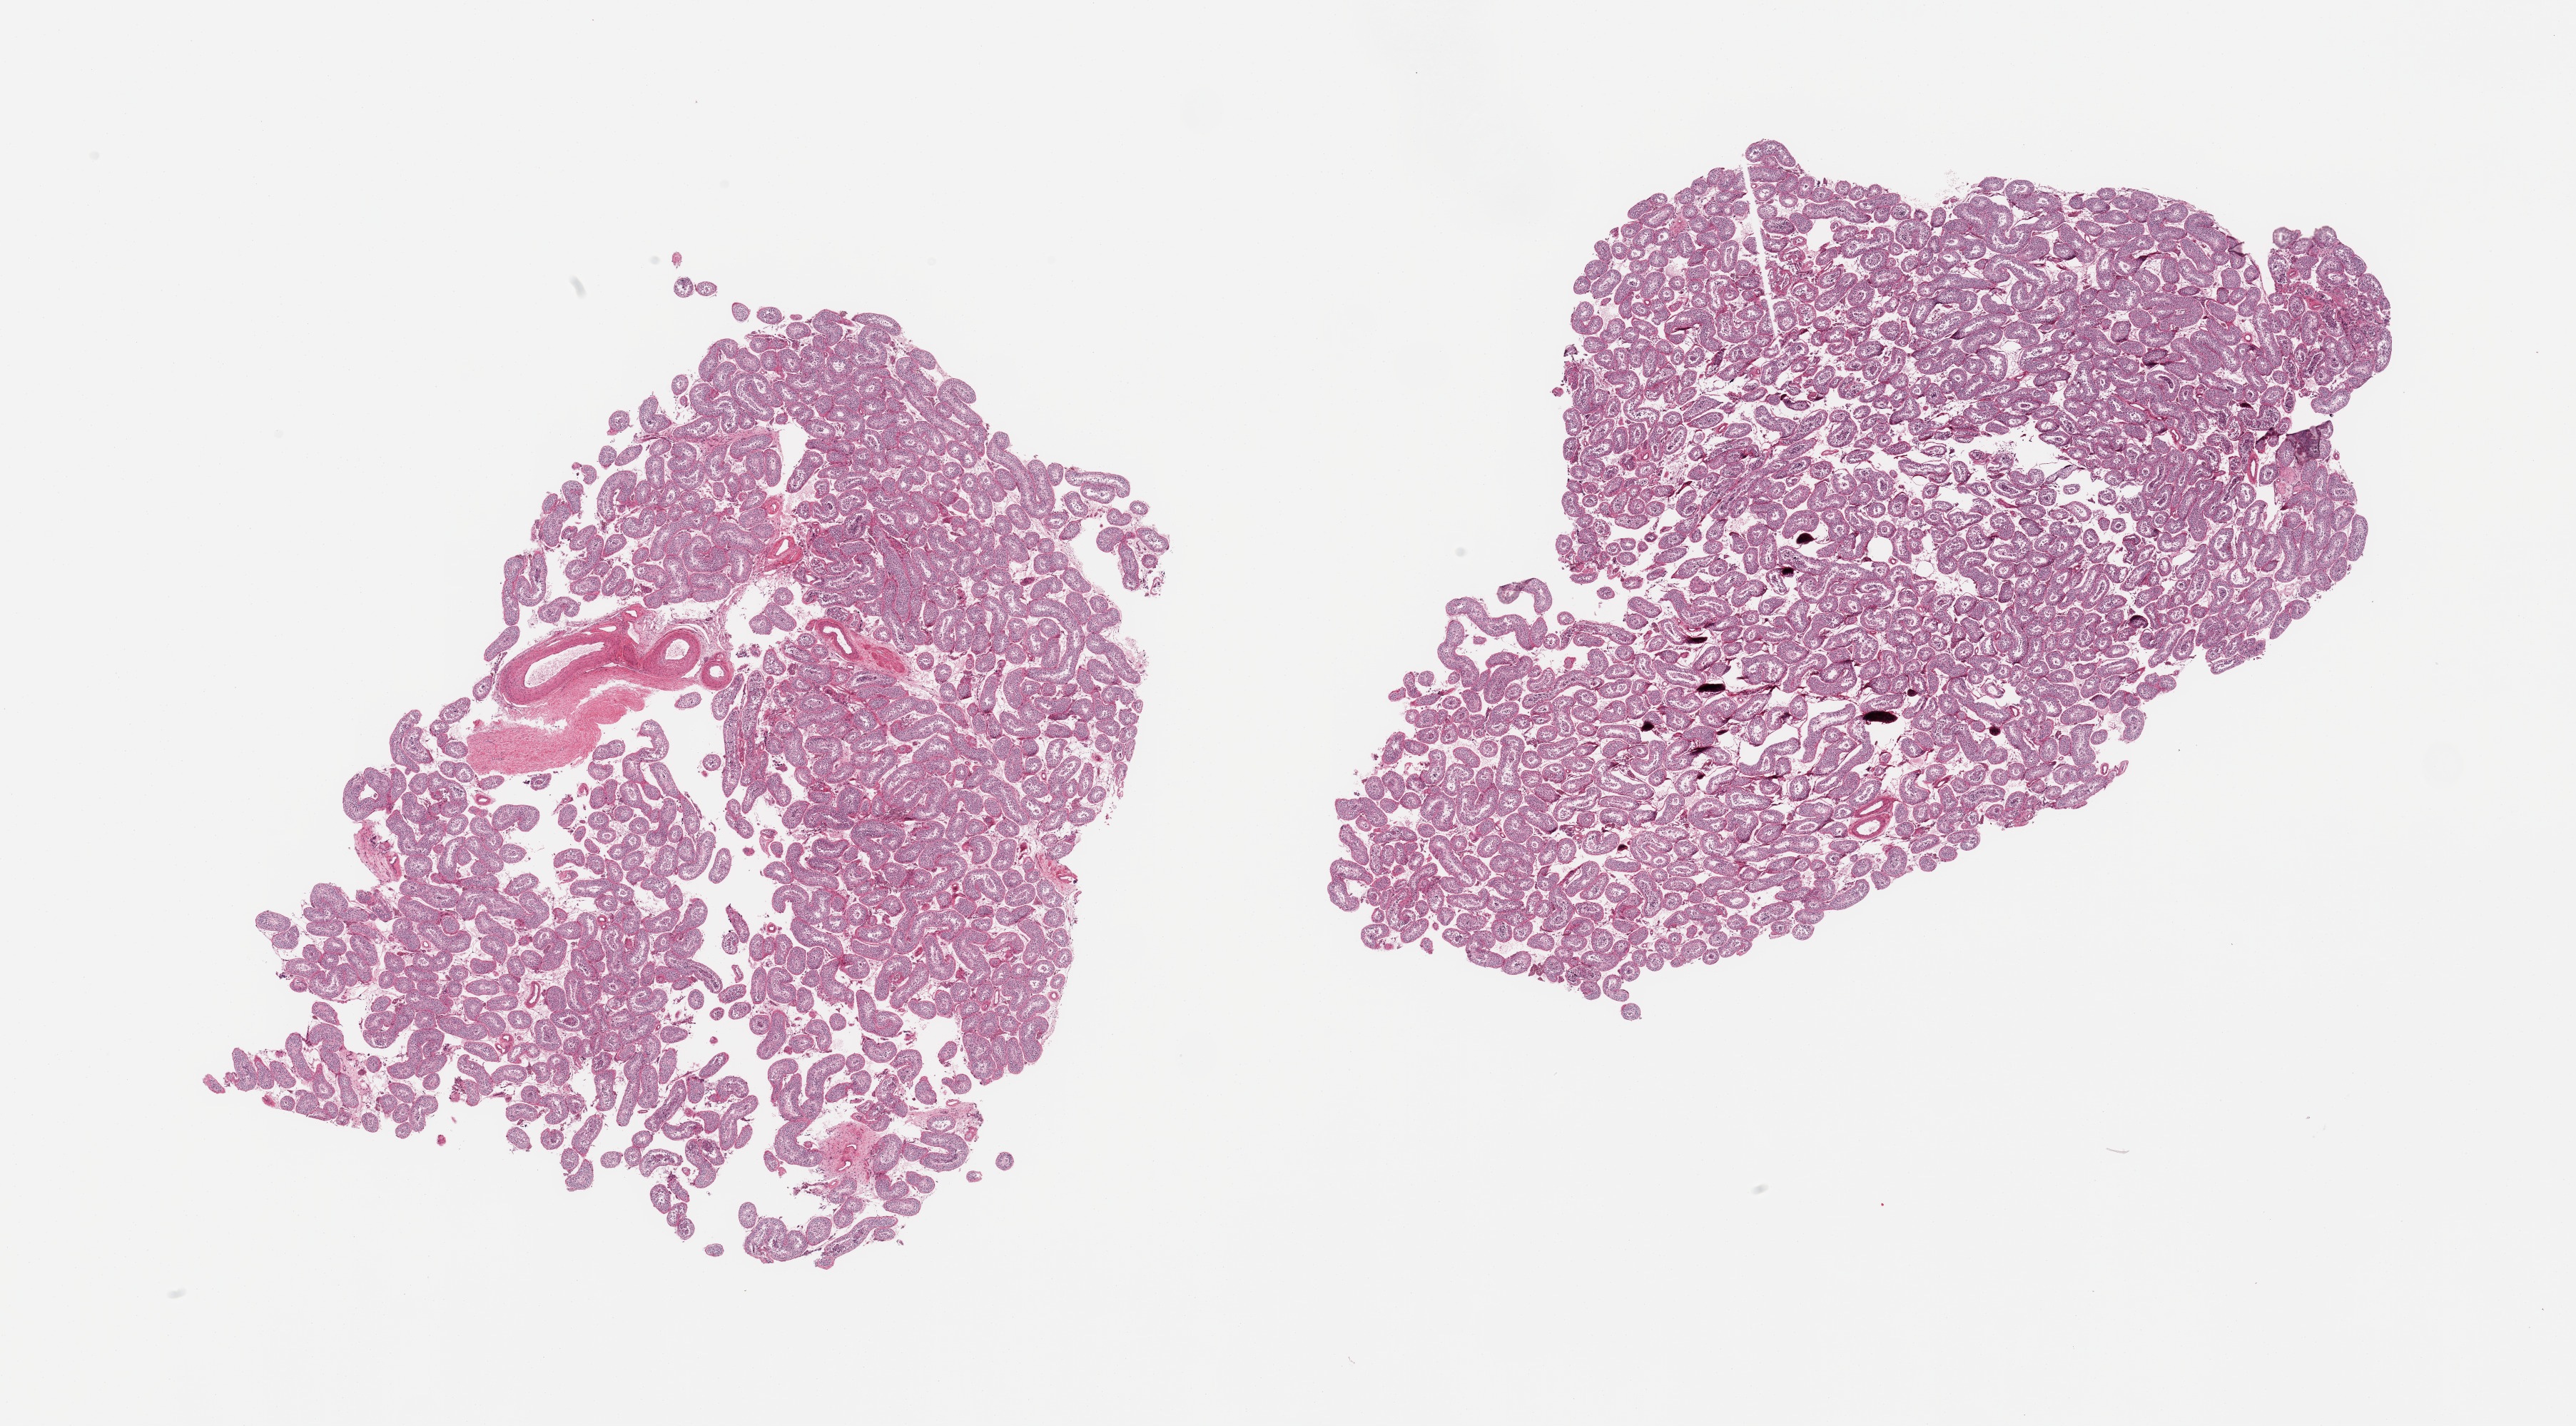
Whole-slide image, H&E stain, whole scanned area (about 28.5 x 15.8 mm) shown as a low-resolution overview, PAXgene-fixed paraffin-embedded (PFPE) section, section of testis (target tissue), donor tissue sample. Donor: male.
Review note (as recorded): 2 pieces, spermatogenesis present but appears reduced. Trace atypical mononculear cells.